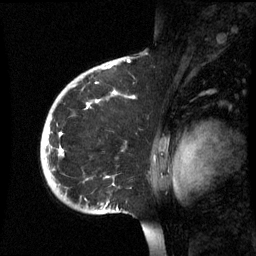
Breast MRI (dynamic contrast-enhanced), one sagittal slice. Slice 43 of 60 in the series (ordered by position). Dynamic contrast-enhanced series, image 2 of 3 at this slice position (ordered by acquisition). 1.5 T. TE 4.2 ms, TR 8.9 ms. 256 × 256 image matrix. Female patient, age 35 years. Case-level facts recorded for this patient, not image findings: setting: breast cancer imaged before/during neoadjuvant chemotherapy; receptor status: HR-positive, HER2-negative.
Outlined on this slice (semi-automatic segmentation, software-assisted and operator-edited):
- analysis volume of interest (the breast-tissue region the enhancement analysis was run in; not a lesion): box from (x=40, y=74) to (x=161, y=215) px
- tumour enhancement mask (voxels above the 70 % enhancement threshold inside the analysis volume of interest): (x=61, y=104)–(x=90, y=155)